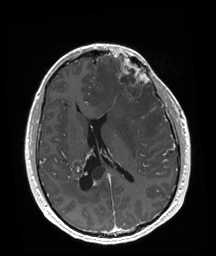
Brain MRI from a brain-tumour surgery series, one axial slice; position 82 of 192 along the scan axis; T1-weighted post-contrast; 1 mm slice thickness; 216 × 256 image matrix. From the clinical record (not read from this slice): tumour location: Left Frontal.
Outlined on this slice (outlined manually by an expert reader):
- tumour: bounding box <117,58,149,103> (left, top, right, bottom; pixels)